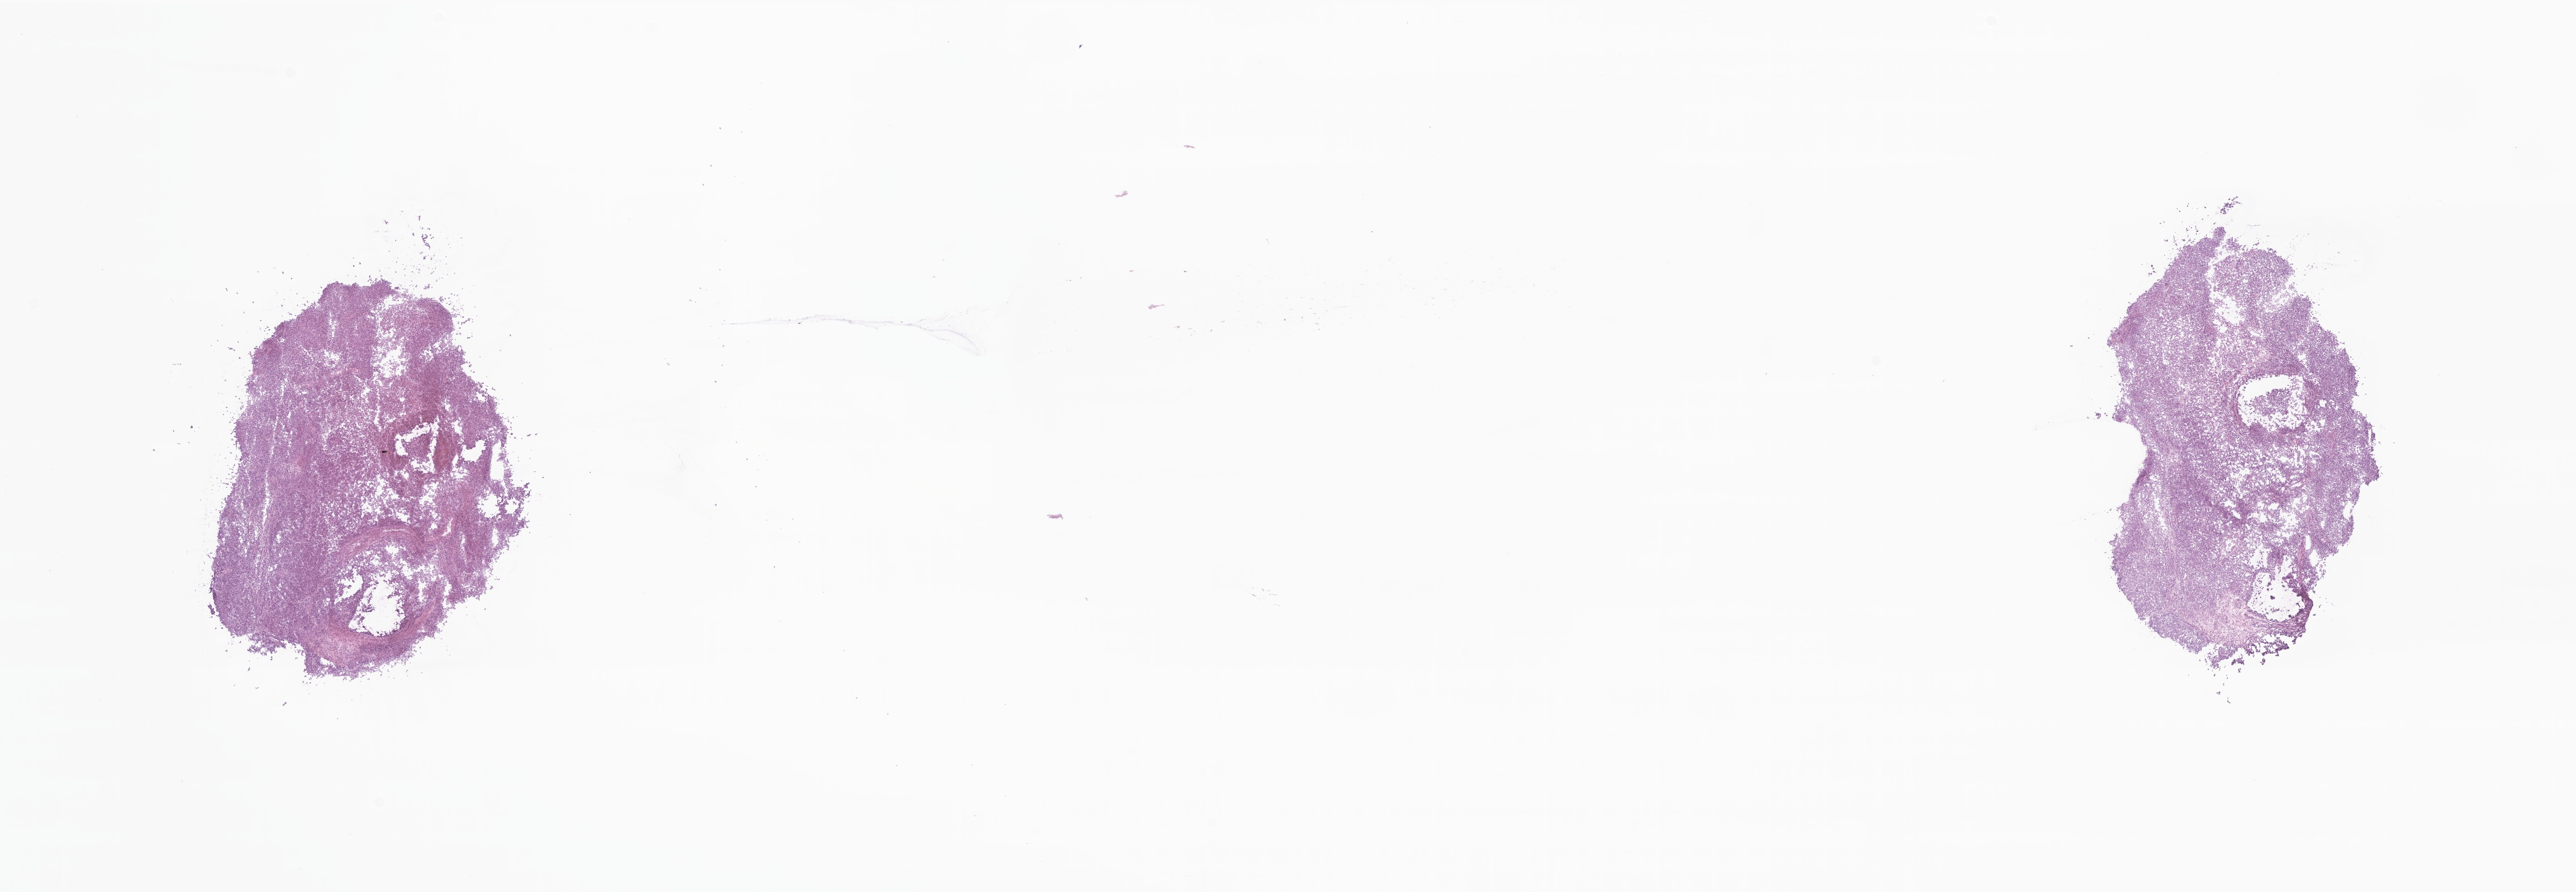
Digitized haematoxylin and eosin-stained section of tumor tissue from the brain, a low-resolution overview of the entire scanned area, about 24.3 x 8.4 mm, frozen section. Female patient, age 403 days (about 1.1 years).
Diagnosis: Neoplasm, uncertain whether benign or malignant.